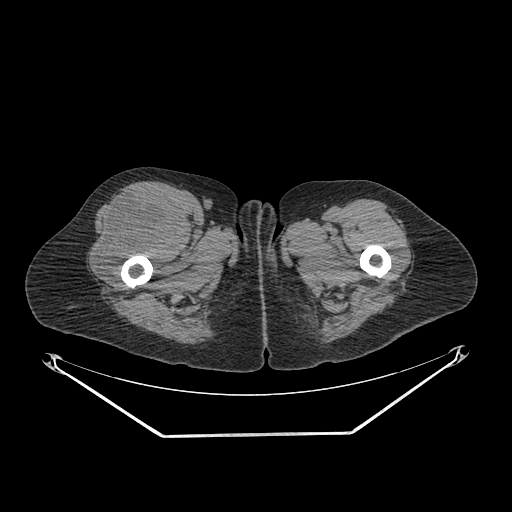
CT of an extremity soft-tissue mass (from a PET/CT study), one axial slice. Slice 270 of 311 in the series (ordered by position). Reconstruction kernel SOFT. 140 kVp. Soft-tissue window (W 400 / L 40 HU). 3.75 mm slice thickness. 512 × 512 image matrix, field of view 500 × 500 mm. Female patient. From the clinical record (not read from this slice): histological type: pleiomorphic undifferentiated sarcoma; grade: high; site of the primary tumour: right quadricep.
Outlined on this slice (expert contour drawn on MRI and transferred to this co-registered scan by the dataset authors):
- tumour plus oedema (research contour): bounding box (x1, y1, x2, y2) in pixels: (96, 190, 182, 275)
- tumour (research contour): (96, 190, 182, 275)